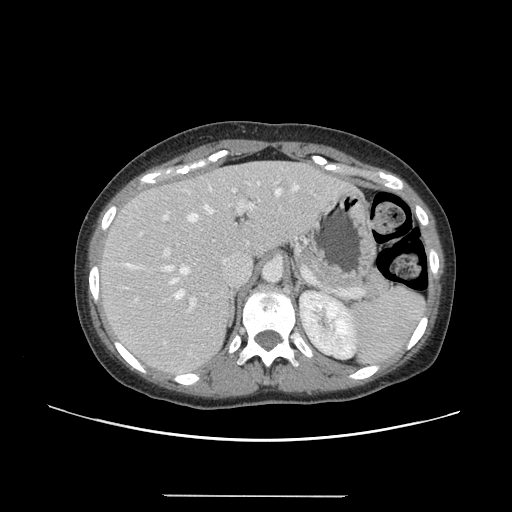
Contrast-enhanced abdominal CT, one axial slice. Slice 98 of 144 in the series (ordered by position). 120 kVp. Soft-tissue window (W 400 / L 40 HU). 512 × 512 image matrix, field of view 380 × 380 mm. Female patient, age 53 years. From the clinical record (not read from this slice): diagnosis: colorectal cancer liver metastases, imaged before liver resection; multiple liver metastases: yes; largest metastasis: 1.1 cm; disease in both lobes: no.
Annotated regions visible in this slice (expert manual segmentation):
- hepatic veins: box from (x=126, y=186) to (x=298, y=298) px
- liver: (x=99, y=162)–(x=346, y=375)
- planned liver remnant (the part of the liver to remain after resection): (x=99, y=162)–(x=306, y=300)
- portal vein (with intrahepatic branches): (x=139, y=182)–(x=278, y=312)